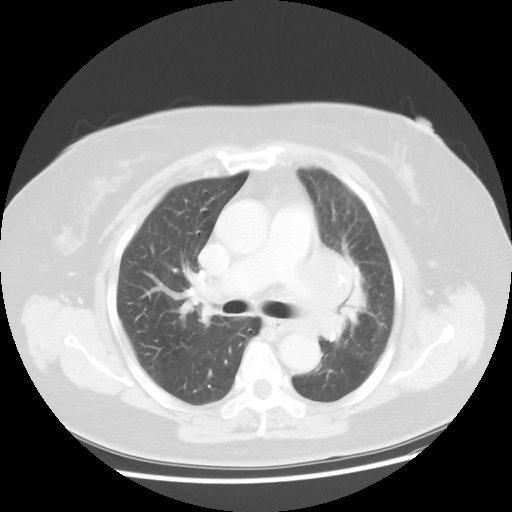
Chest CT, one axial slice; slice 28 of 49 in the series (ordered by position); reconstruction kernel STANDARD; 120 kVp; lung window (W 1500 / L -600 HU); 5 mm slice thickness; 512 × 512 image matrix, field of view 374 × 374 mm. Patient: female, 58 years. Case-level facts recorded for this patient, not image findings: clinical TNM (as recorded): T4 N3 M0; histopathological grade: G3.
Structures marked on this image (bounding box drawn by a radiologist):
- lung tumour (recorded histology: small cell carcinoma): bounding box [x1, y1, x2, y2] px = [278, 241, 360, 346]